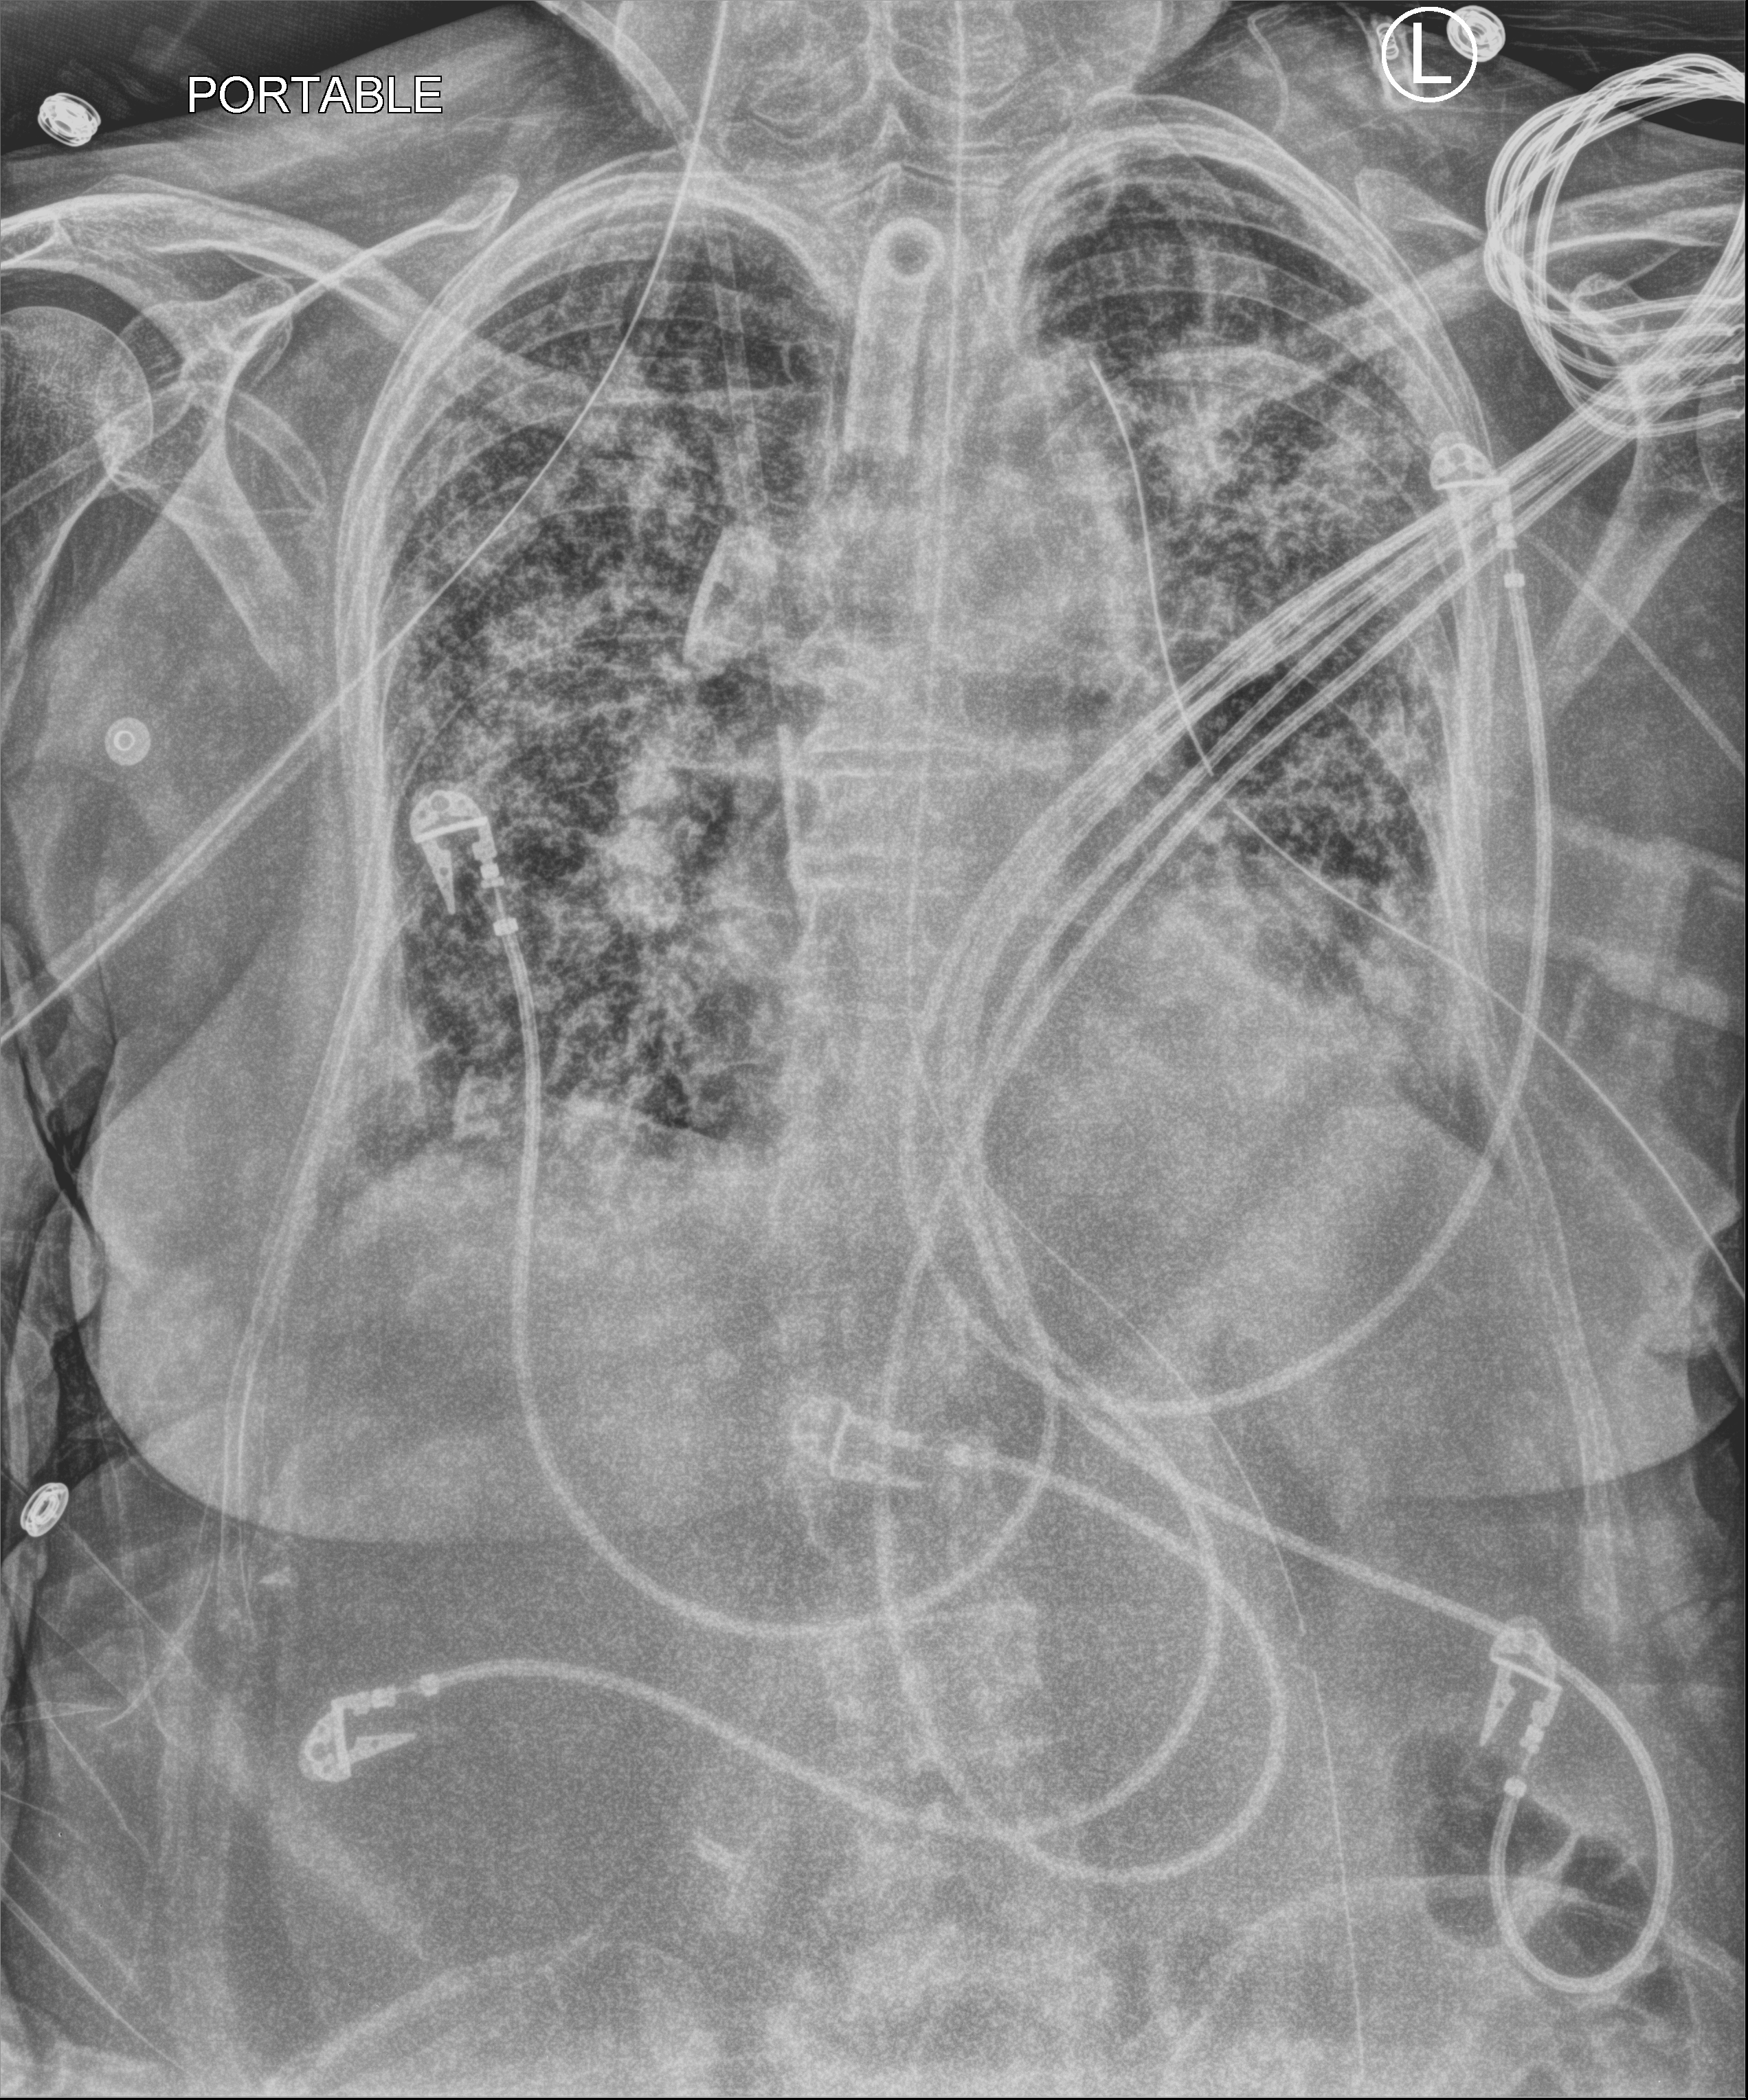
Bedside chest radiograph (computed radiography), anteroposterior (AP) projection. Patient hospitalised with COVID-19; female, aged 75–90 years.
Hospital-stay facts (about this admission, not read from this image; timing relative to this image not recorded): admitted to intensive care during this hospital stay: yes; mechanically ventilated during this hospital stay: yes; hypertension (admission record): yes.